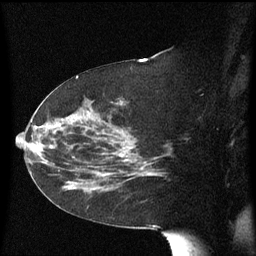
Breast MRI (dynamic contrast-enhanced), one sagittal slice. Slice 32 of 60 in the series (ordered by position). Dynamic contrast-enhanced series, image 2 of 3 at this slice position (ordered by acquisition). 1.5 T. TE 4.2 ms, TR 8.4 ms. 2.3 mm slice thickness. 256 × 256 image matrix, field of view 200 × 200 mm. Female patient, age 63 years. Case-level facts recorded for this patient, not image findings: setting: breast cancer imaged before/during neoadjuvant chemotherapy; receptor status: HER2-positive.
Outlined on this slice (semi-automatic segmentation, software-assisted and operator-edited):
- analysis volume of interest (the breast-tissue region the enhancement analysis was run in; not a lesion): bounding box [x1, y1, x2, y2] px = [63, 144, 147, 194]
- tumour enhancement mask (voxels above the 70 % enhancement threshold inside the analysis volume of interest): [98, 147, 130, 176]